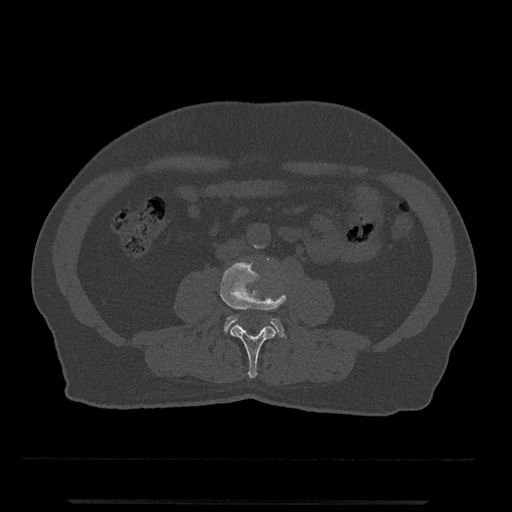
CT including the spine, one axial slice. Position 181 of 797 along the scan axis. Reconstruction kernel Br40s/3. Bone window (W 1800 / L 400 HU). 512 × 512 image matrix, field of view 419 × 419 mm. Patient: male, 63 years. Case-level facts recorded for this patient, not image findings: primary cancer: prostate.
Annotated regions visible in this slice (semi-automatic segmentation, software-assisted and operator-edited):
- L3 vertebra: box from (x=220, y=261) to (x=286, y=379) px
- L4 vertebra: (x=224, y=316)–(x=285, y=337)